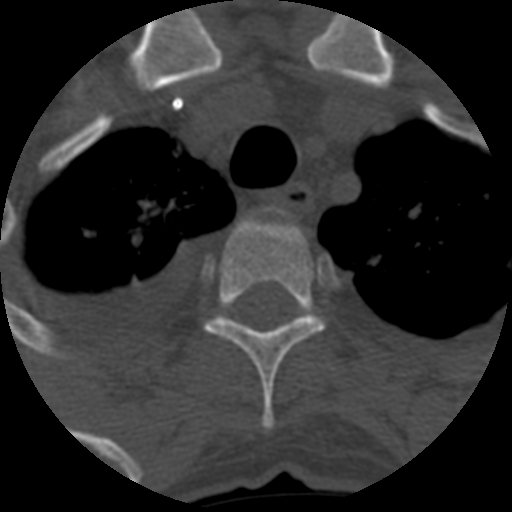
CT including the spine, one axial slice; position 488 of 708 along the scan axis; 120 kVp; one of 3 acquisitions stored at this slice position; bone window (W 1800 / L 400 HU); 1.25 mm slice thickness; 512 × 512 image matrix, field of view 160 × 160 mm. Patient age 55 years. From the clinical record (not read from this slice): primary cancer: colon.
Annotated regions visible in this slice (semi-automatically segmented with operator editing):
- T3 vertebra: bounding box (x1, y1, x2, y2) in pixels: (205, 214, 324, 430)
- T4 vertebra: (290, 315, 309, 325)